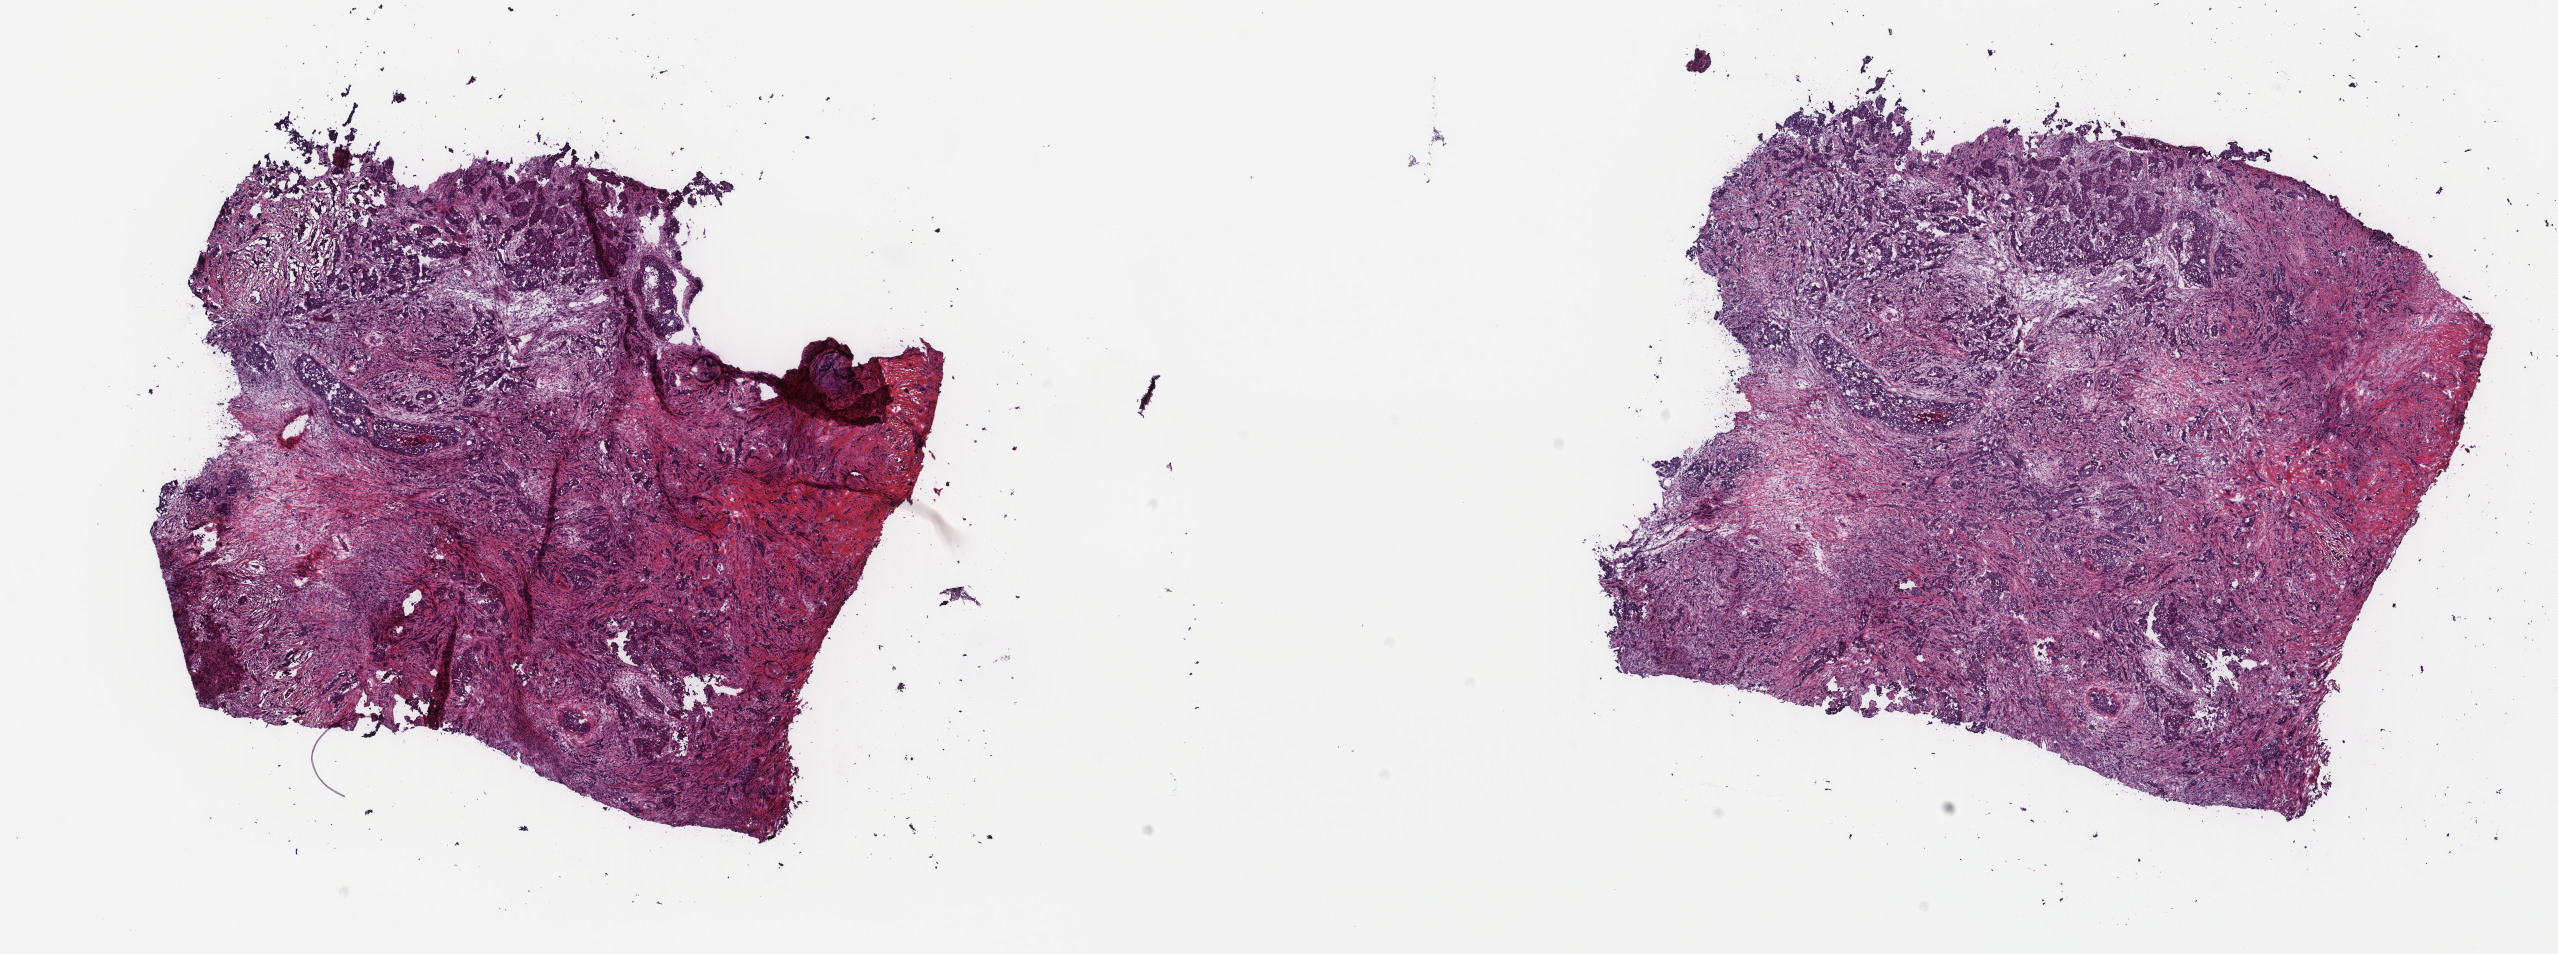
Digitized H&E tissue section (whole slide) — low-resolution overview of the scanned area, about 20.3 x 7.6 mm (acquisition: 40x scan). Frozen section. Primary tumour sample from the breast. Female patient; age at initial diagnosis 41 years. Pathologist review of this section (percent, as recorded): tumour cells 95%, tumour nuclei 70%, normal cells 0%, stromal cells 5%, necrosis 0%. Inflammatory infiltration, as recorded: lymphocyte infiltration 0%, monocyte infiltration 0%, neutrophil infiltration 0%.
* AJCC pathologic stage: IIB
* histologic diagnosis: Infiltrating duct carcinoma, NOS
* TNM: T2 N1a M0
* lymph nodes positive (case pathology): 3 of 14 examined